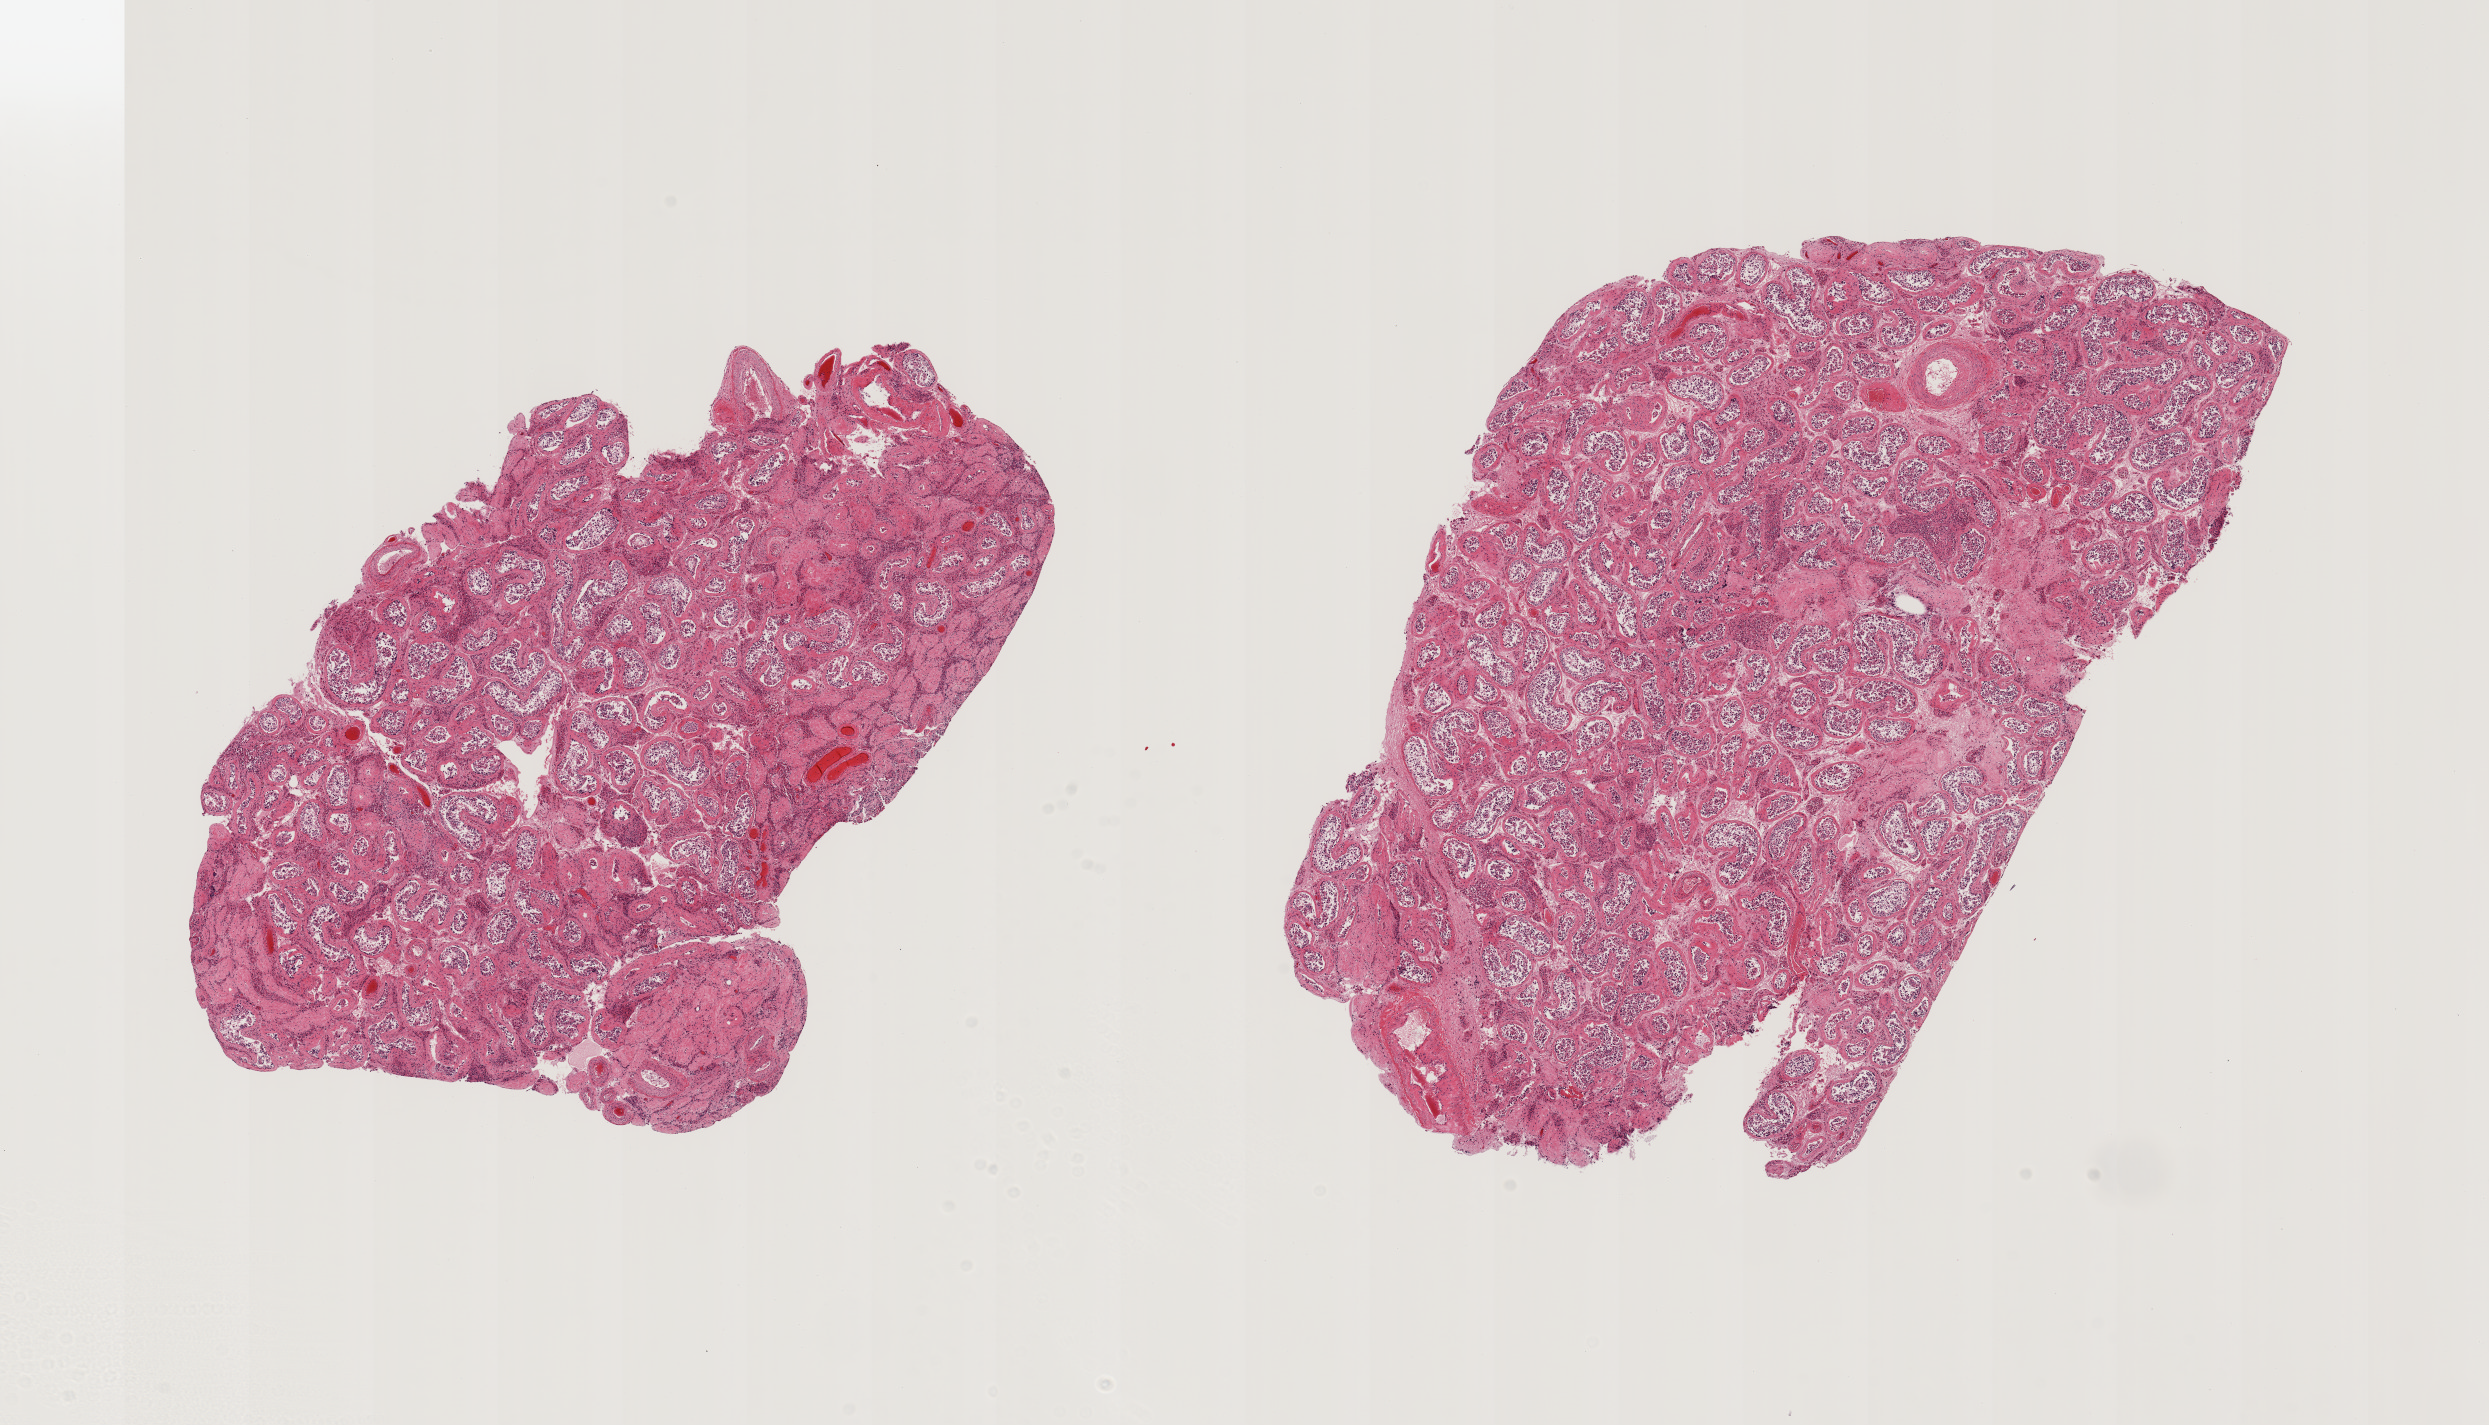
Digitized H&E-stained section — a low-resolution overview of the entire scanned area, about 19.7 x 11.3 mm. PAXgene-fixed paraffin-embedded (PFPE) section. Section of testis (target tissue). Donor tissue sample. Donor sex: male.
Pathologist's review note for this sample: 2 pieces; reduced spermatogenesis; 1 piece has 20% hyalinized tubules and Leydig cell hyperplasia.